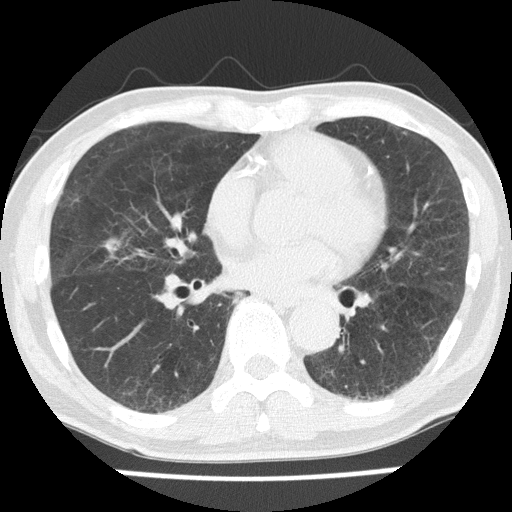
Low-dose screening chest CT, axial slice, first (baseline) screen, lung window (W 1500 / L -600 HU), 2 mm slice thickness, lung (sharp) reconstruction kernel (FC51), 120 kVp, slice 97 of 169 in the series. Male, age 68 years at enrolment. Current smoker at enrolment.
Expert-annotated lung lesion, bounding box [x1, y1, x2, y2] px = [46, 183, 90, 217]. No non-calcified nodule or mass ≥4 mm was recorded by the screening reader at this exam. Lung cancer was diagnosed 386 days after this screen: squamous cell carcinoma, NOS, right upper lobe, moderately differentiated (G2), stage IA (AJCC 6th edition), 10 mm at pathology.